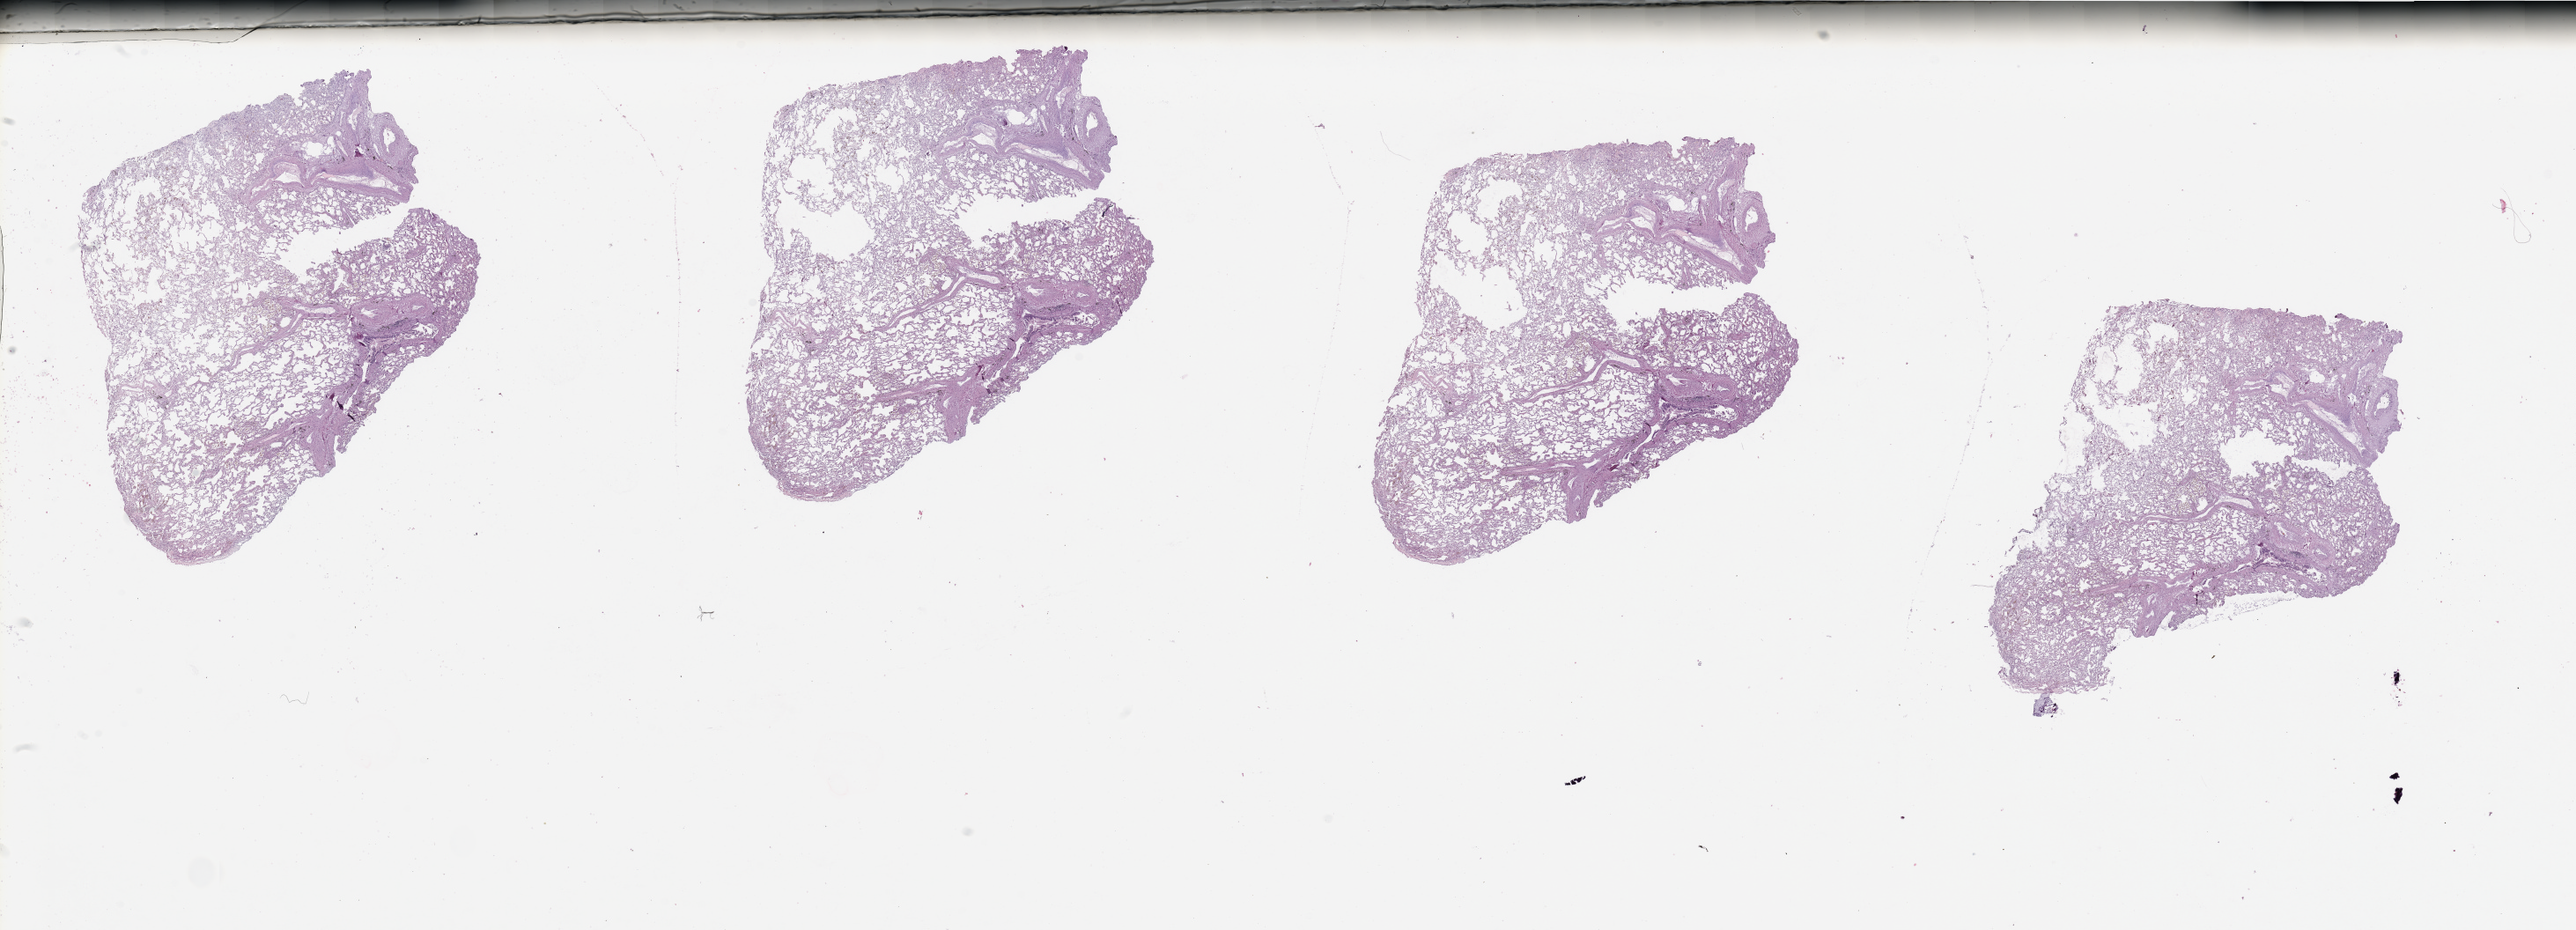
Digitized Hematoxylin and eosin (H&E) stained tissue section (whole slide) — whole scanned area (about 46.3 x 16.7 mm) shown as a low-resolution overview, lung, normal (non-tumour) tissue. Male, 51 y/o.
This section: normal (non-tumour) tissue from the same patient. Patient diagnosis: Adenocarcinoma, NOS.